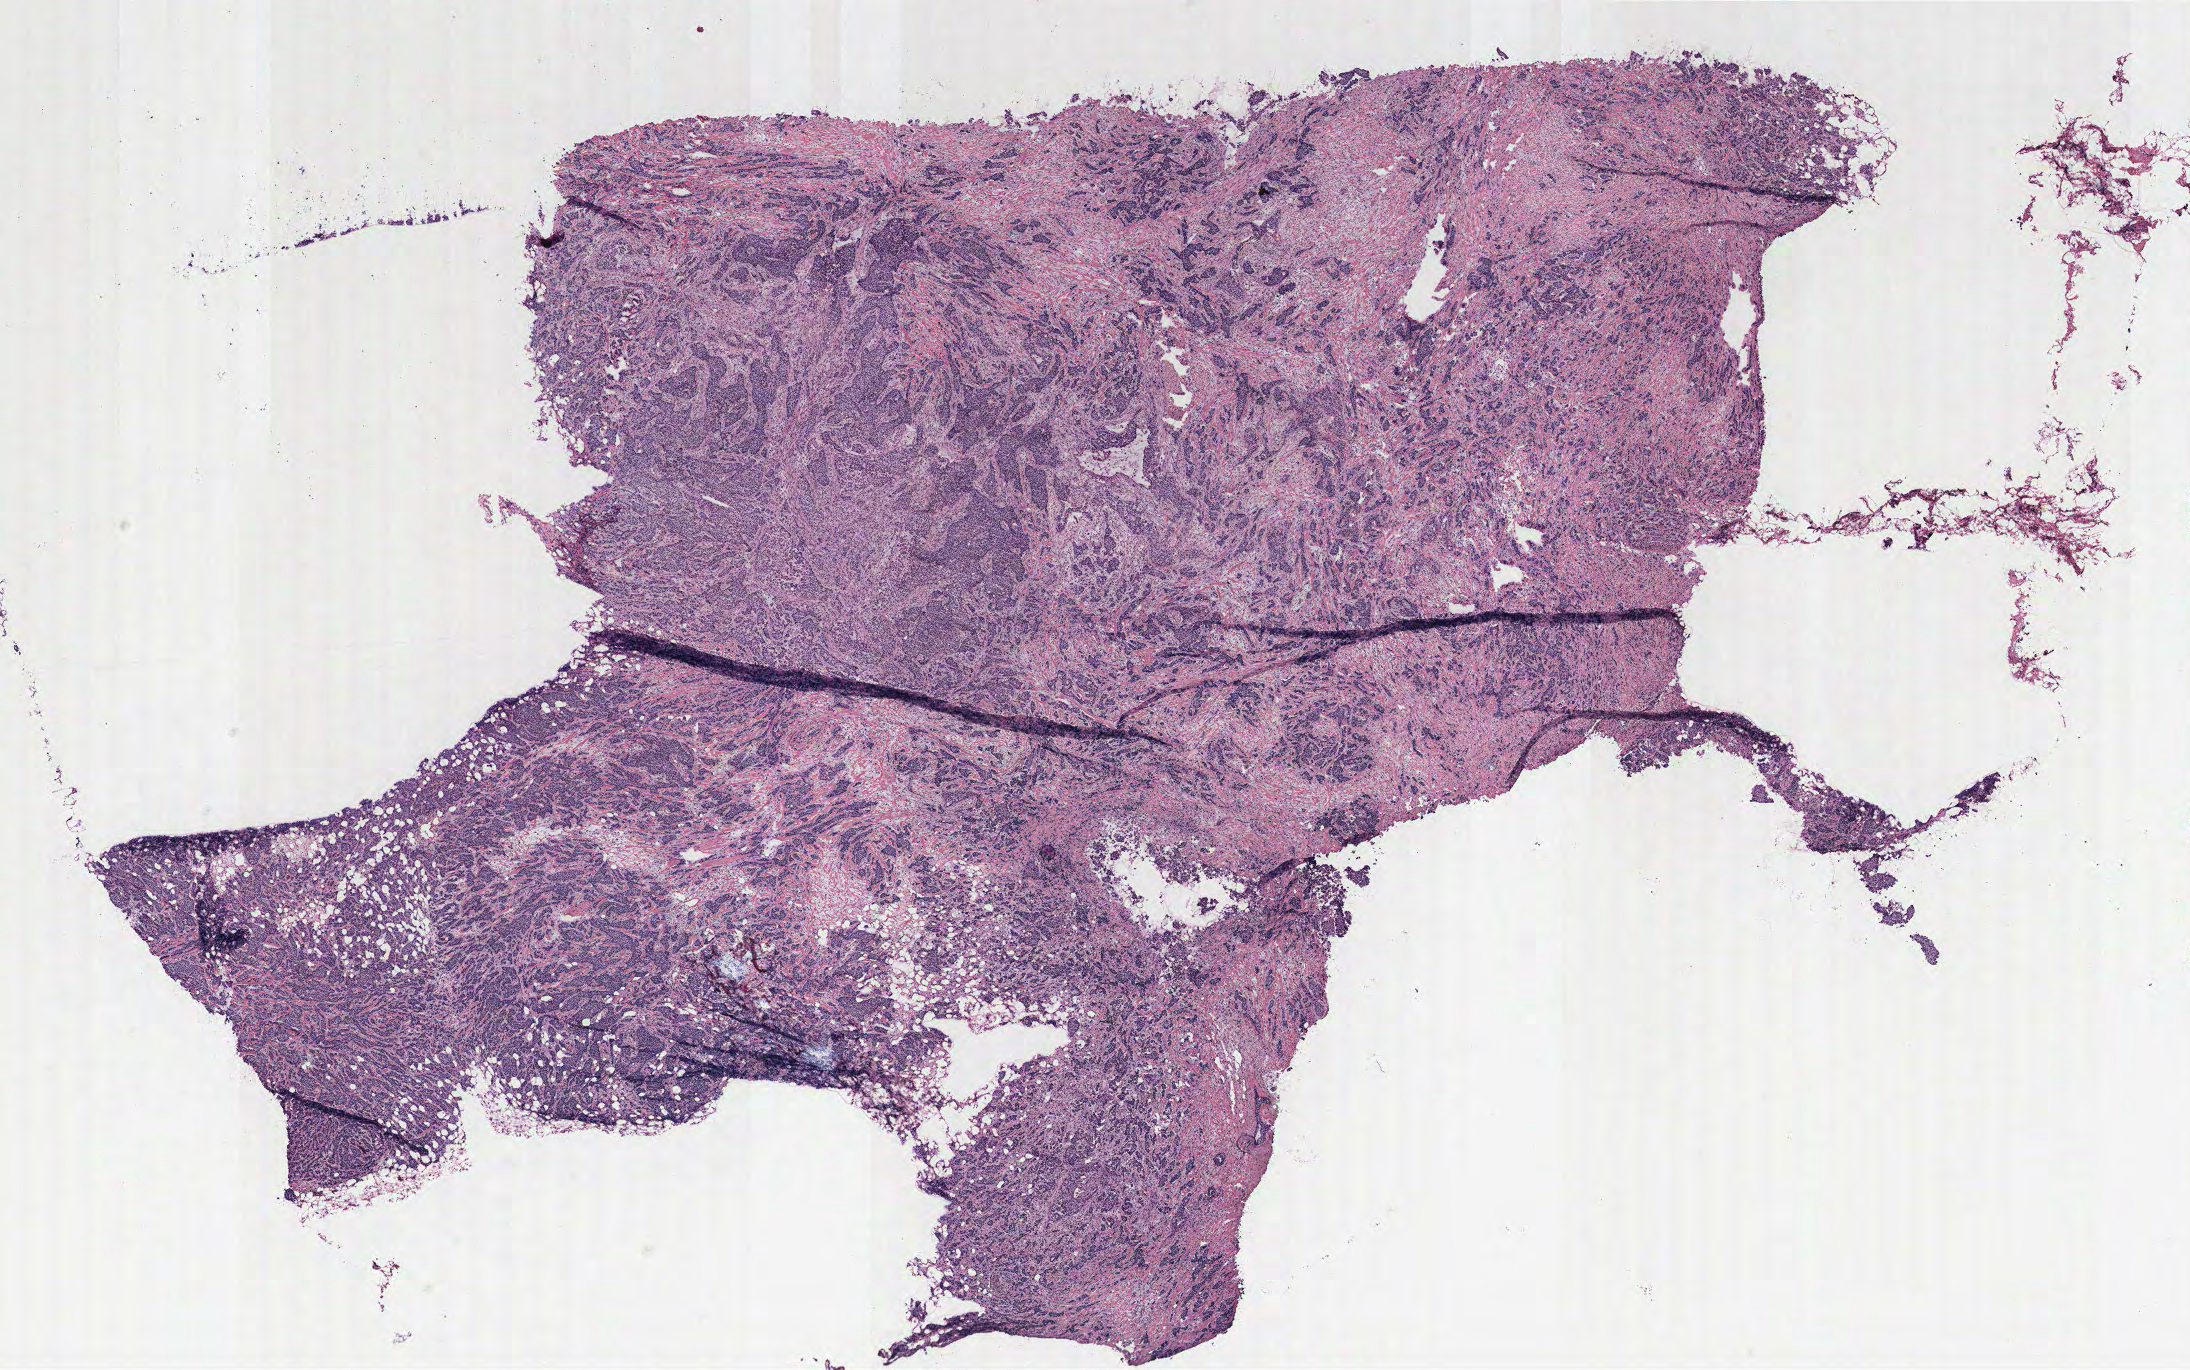
H&E whole-slide image, low-resolution overview of the scanned area, about 17.5 x 11.0 mm. Breast, tumour tissue. Patient: female, age 38 years.
• AJCC pathologic stage: IIB
• diagnosis: Infiltrating duct carcinoma, NOS